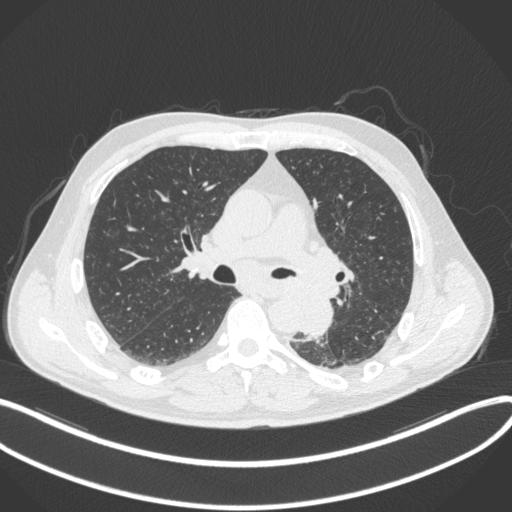
Chest CT, one axial slice. 120 kVp. Lung window (W 1500 / L -600 HU). 1 mm slice thickness. 512 × 512 image matrix, field of view 400 × 400 mm. Patient: male, 59 years. From the clinical record (not read from this slice): clinical TNM (as recorded): T2a N2 M0.
Structures marked on this image (rectangle marked by the reading radiologist):
- lung tumour (recorded histology: squamous cell carcinoma): bounding box (x1, y1, x2, y2) in pixels: (297, 286, 337, 341)